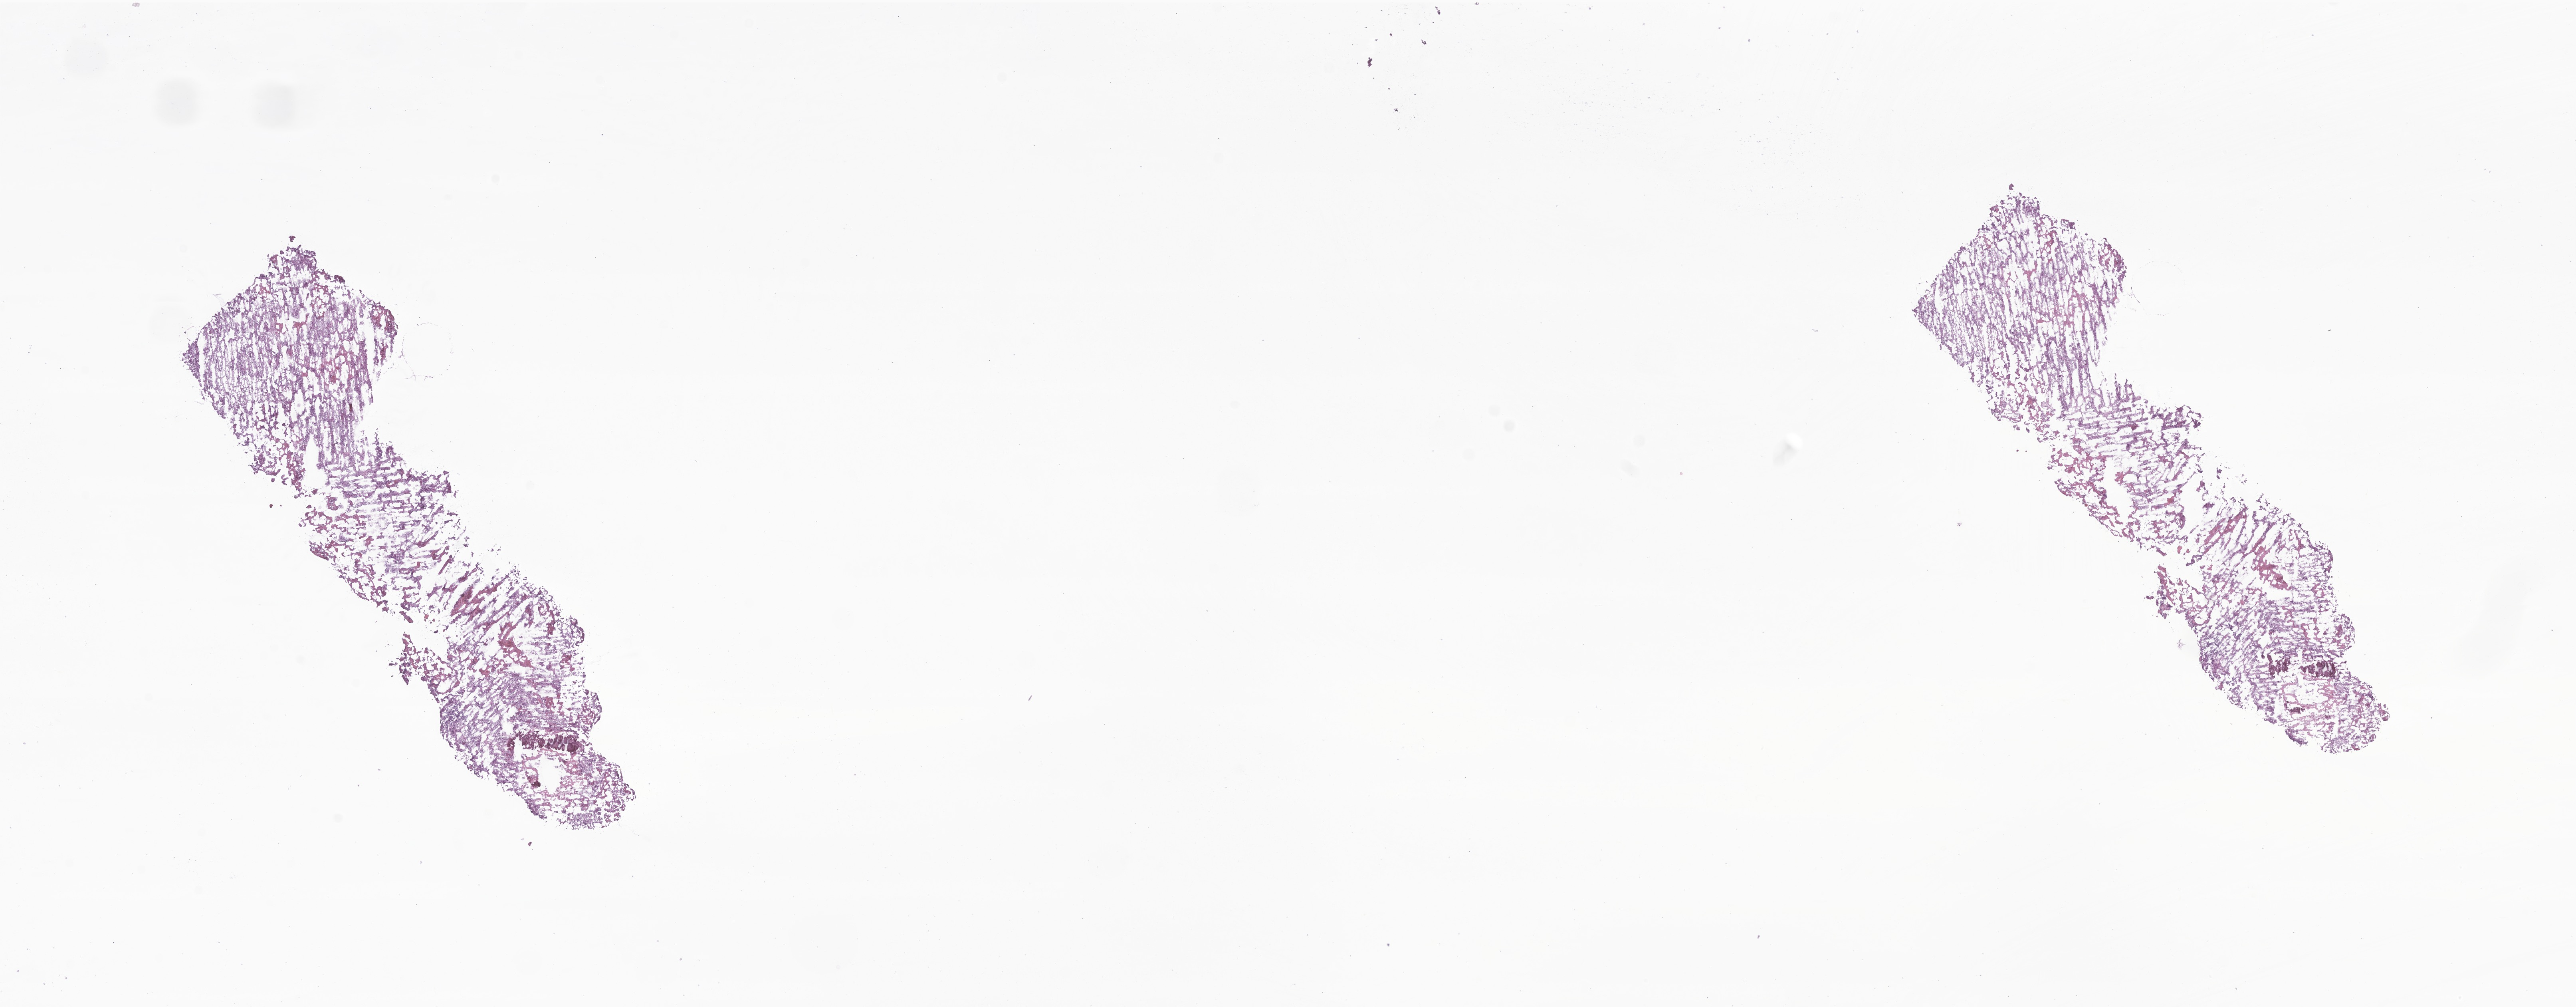
Digitized H&E-stained section of tumor tissue from the brain, low-resolution overview of the scanned area, about 27.2 x 10.6 mm. Cryosection (OCT / tissue freezing medium). Female patient, age 587 days (about 1.6 years).
* diagnosis: Neoplasm, malignant